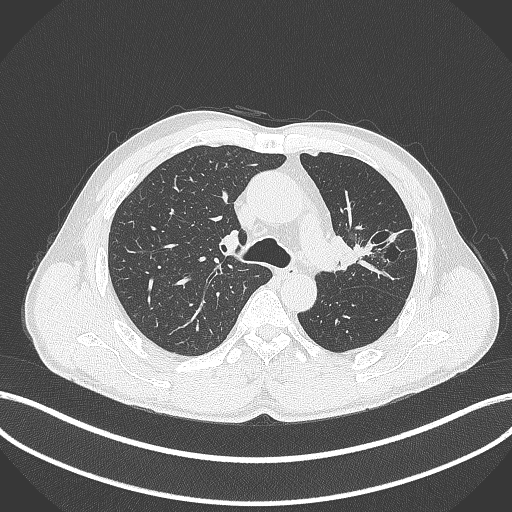
Chest CT, one axial slice; position 279 of 429 along the scan axis; reconstruction kernel B70f; lung window (W 1500 / L -600 HU); 512 × 512 image matrix. Male patient, age 57 years. From the clinical record (not read from this slice): clinical TNM (as recorded): T2b N0 M0.
Structures marked on this image (bounding box drawn by a radiologist):
- lung tumour (recorded histology: squamous cell carcinoma): bounding box (x1, y1, x2, y2) in pixels: (329, 232, 390, 275)